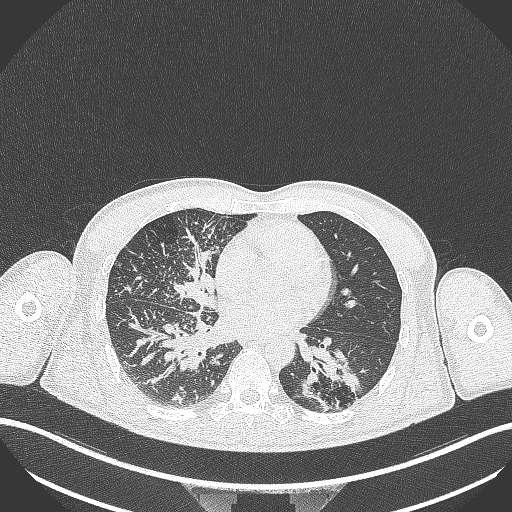
Chest CT, one axial slice. Position 139 of 348 along the scan axis. Reconstruction kernel B70f. 120 kVp. Lung window (W 1500 / L -600 HU). 1 mm slice thickness. 512 × 512 image matrix, field of view 400 × 400 mm. Patient: male, 49 years. From the clinical record (not read from this slice): clinical TNM (as recorded): T2b N1 M0.
Outlined on this slice (rectangle marked by the reading radiologist):
- lung tumour (recorded histology: adenocarcinoma): box from (x=296, y=340) to (x=365, y=411) px